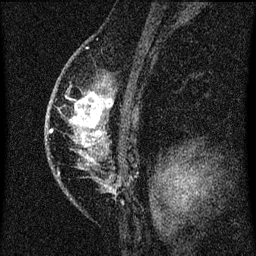
Breast MRI (dynamic contrast-enhanced), one sagittal slice; position 46 of 60 along the scan axis; dynamic contrast-enhanced series, image 2 of 3 at this slice position (ordered by acquisition); 1.5 T; TE 4.2 ms, TR 8 ms; 2 mm slice thickness; 256 × 256 image matrix. Patient: female, 46 years.
Outlined on this slice (semi-automatic segmentation, software-assisted and operator-edited):
- analysis volume of interest (the breast-tissue region the enhancement analysis was run in; not a lesion): bounding box <54,70,114,195> (left, top, right, bottom; pixels)
- tumour enhancement mask (voxels above the 70 % enhancement threshold inside the analysis volume of interest): <70,92,112,159>